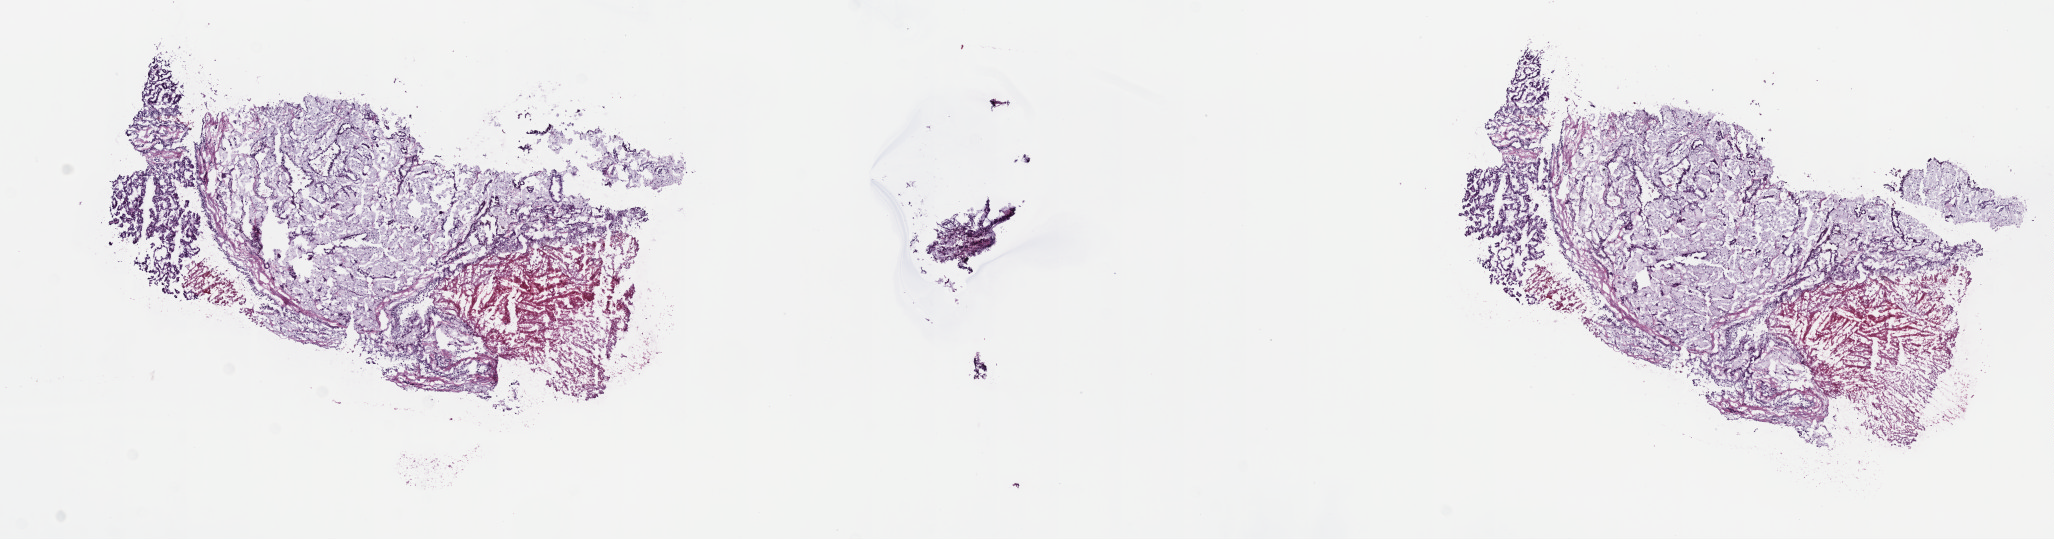
H&E whole-slide image, shown as a low-resolution overview of the whole scanned area (about 16.6 x 4.4 mm, slide scanned at 40x); frozen section; sample: primary tumour, kidney. Patient: male, age at initial diagnosis 80 years. Pathologist review of this section (percent, as recorded): tumour cells 27%, tumour nuclei 60%, normal cells 0%, stromal cells 55%, necrosis 18%. Infiltration values recorded for this section: lymphocyte infiltration 2%, monocyte infiltration 35%, neutrophil infiltration 0%.
* histologic diagnosis: Papillary adenocarcinoma, NOS
* AJCC pathologic stage: II (6th edition)